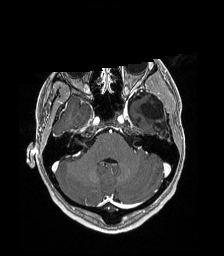
Brain MRI from a brain-tumour surgery series, one axial slice; slice 132 of 192 in the series (ordered by position); T1-weighted post-contrast; 1 mm slice thickness; 224 × 256 image matrix, field of view 224 × 256 mm. From the clinical record (not read from this slice): histopathology: Low grade glioma; IDH mutation: no; tumour location: Left Parieto-Occipital Intraventricular.
Annotated regions visible in this slice (outlined manually by an expert reader):
- previous resection cavity: bounding box <142,98,168,137> (left, top, right, bottom; pixels)